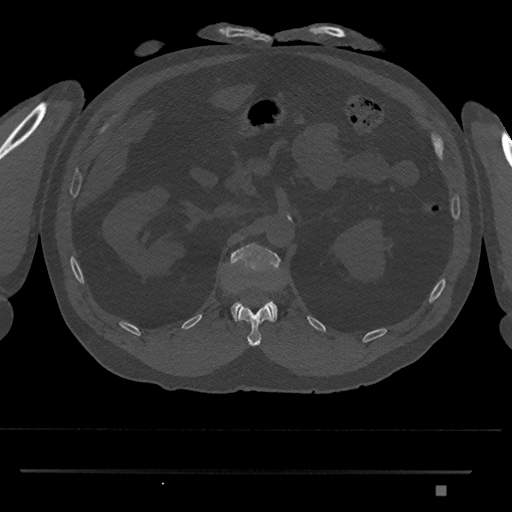
CT including the spine, one axial slice. Slice 858 of 1134 in the series (ordered by position). 120 kVp. Bone window (W 1800 / L 400 HU). 0.5 mm slice thickness. 512 × 512 image matrix. Patient: male, 65 years. From the clinical record (not read from this slice): primary cancer: prostate.
Annotated regions visible in this slice (semi-automatically segmented with operator editing):
- L1 vertebra: bounding box [x1, y1, x2, y2] px = [228, 243, 281, 322]
- T12 vertebra: [237, 304, 272, 346]